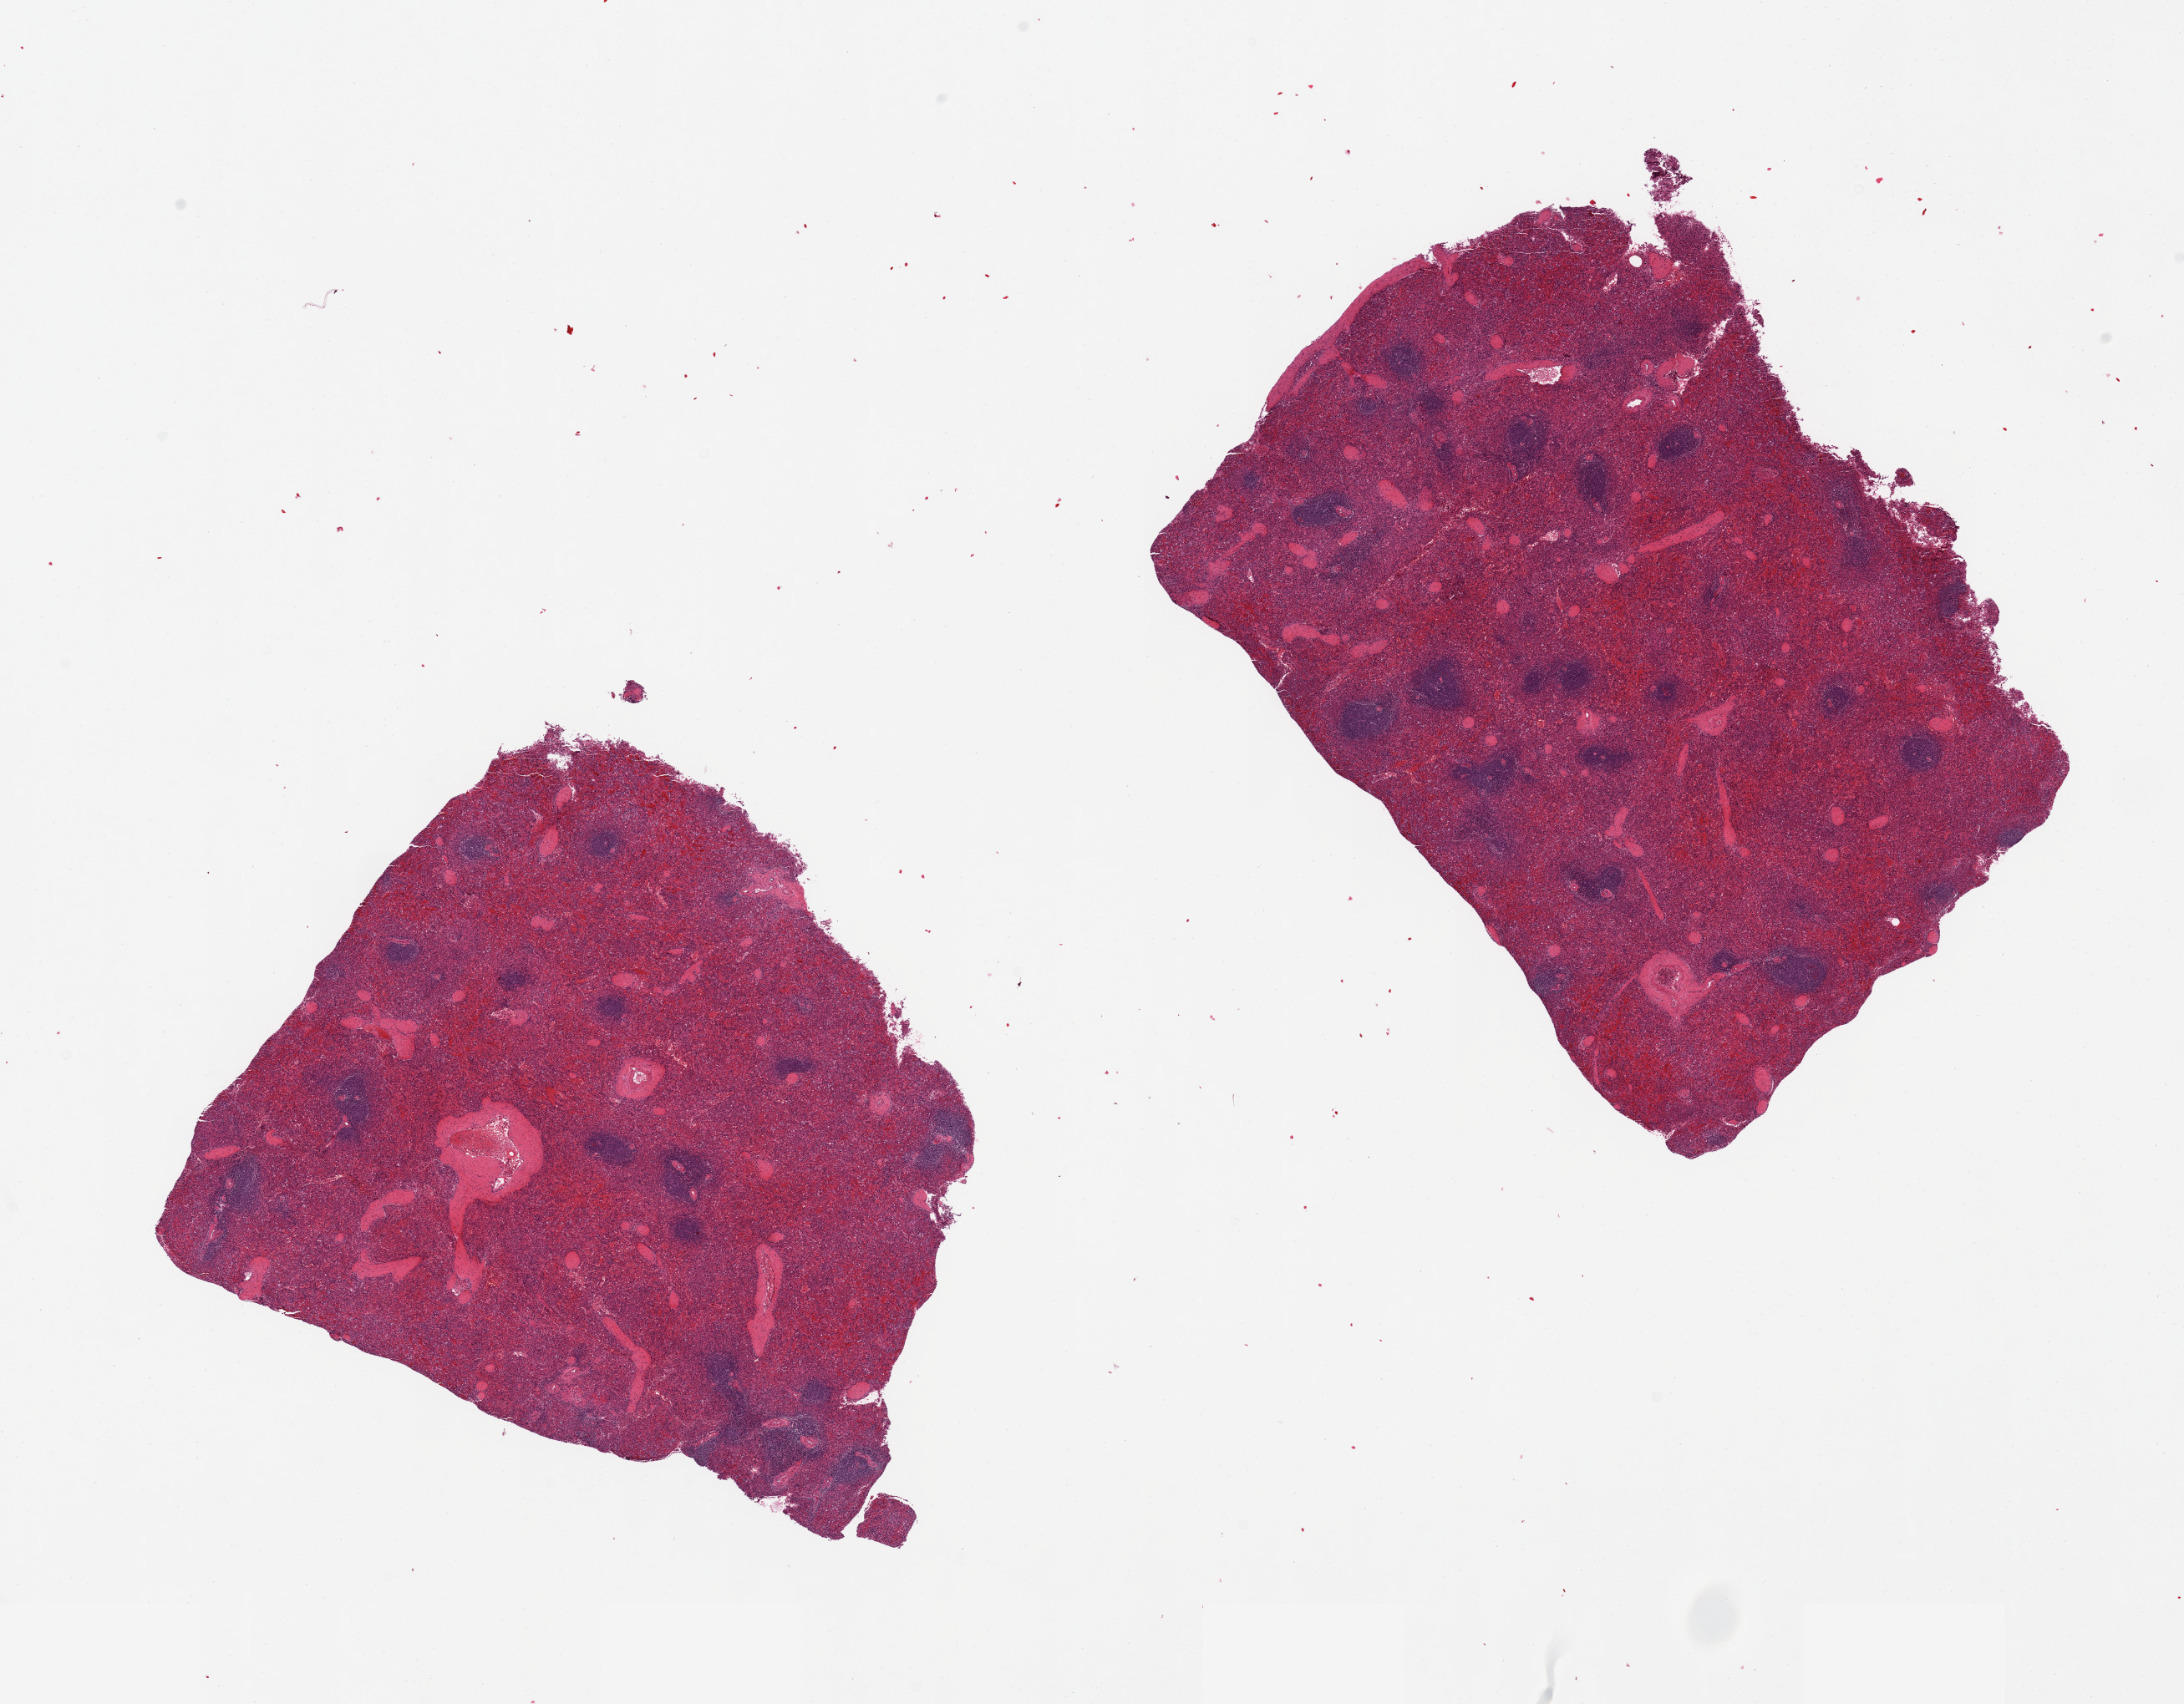
Digitized haematoxylin and eosin-stained section — low-resolution overview of the scanned area, about 20.7 x 16.1 mm (from a 20x scan), PAXgene-fixed, paraffin-embedded tissue, target tissue: spleen, tissue donor sample. Donor sex: male.
Review note (as recorded): 2 pieces; slight congestion.